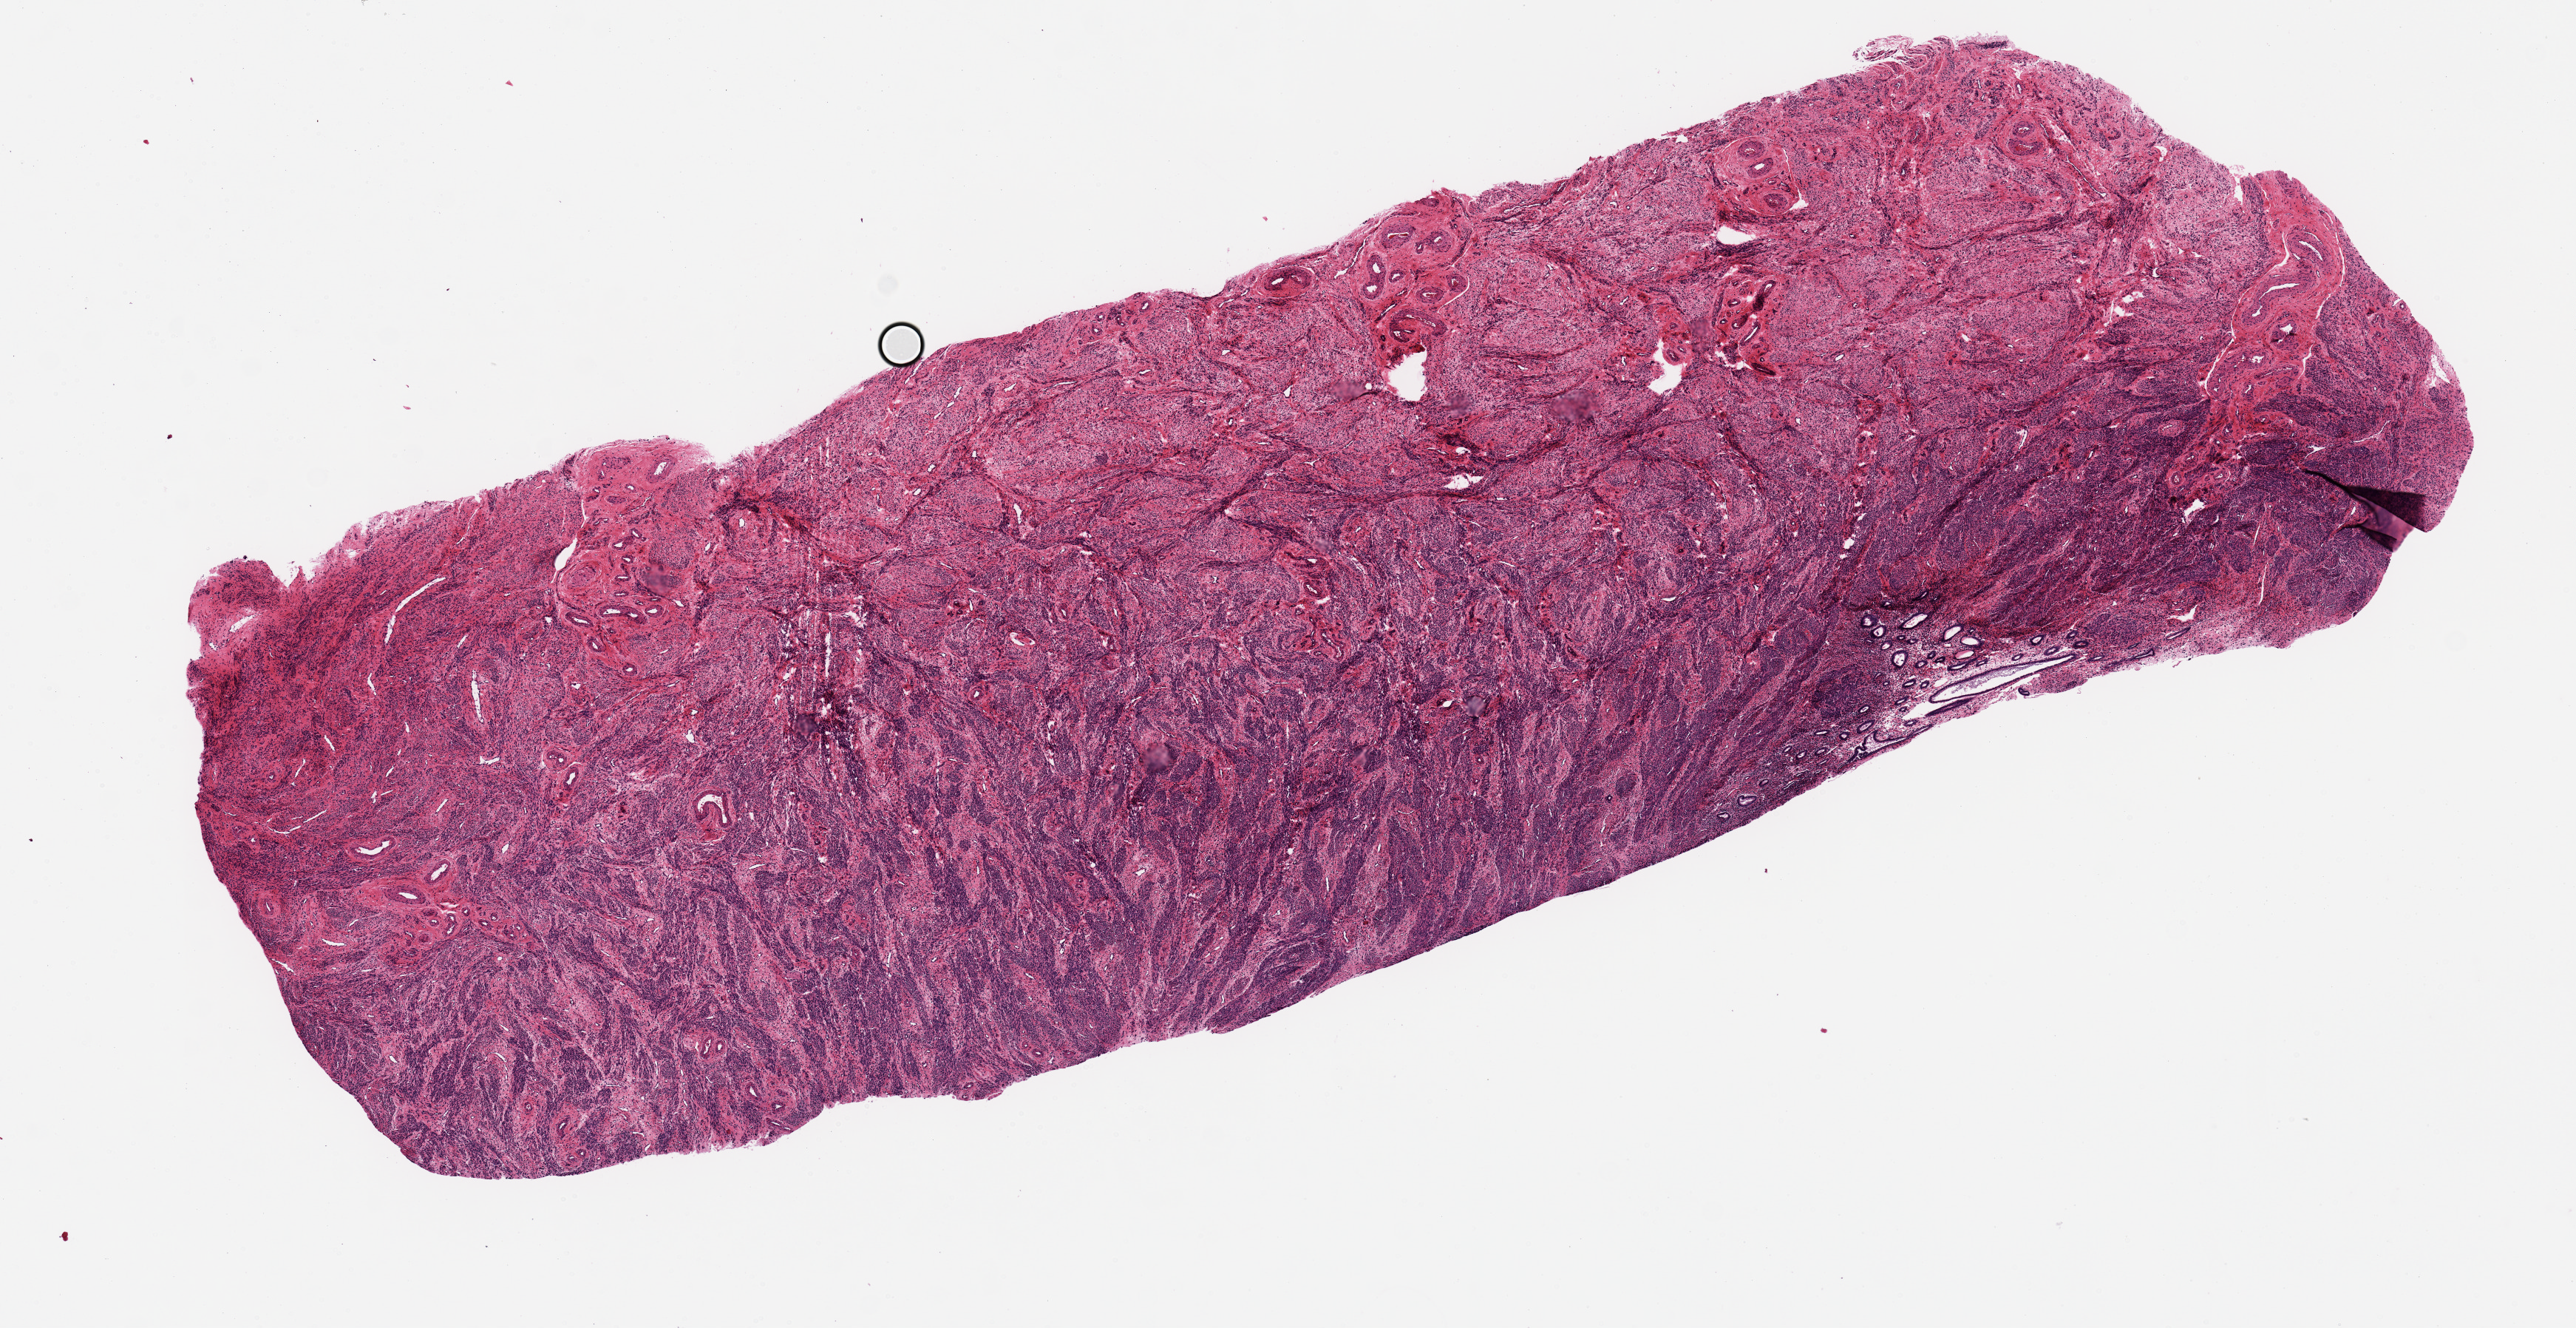
Digitized hematoxylin and eosin (H&E)-stained section, shown as a low-resolution overview of the whole scanned area (about 13.8 x 7.1 mm). PAXgene-fixed paraffin-embedded (PFPE) section. Sampled site (target tissue): uterus. Donor tissue sample. Female donor.
Review note (as recorded): small number of glands.